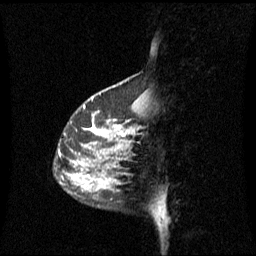
Breast MRI (dynamic contrast-enhanced), one sagittal slice; slice 19 of 60 in the series (ordered by position); dynamic contrast-enhanced series, image 2 of 3 at this slice position (ordered by acquisition); 1.5 T; TE 4.2 ms, TR 8.4 ms; 256 × 256 image matrix, field of view 240 × 240 mm. Patient: female, 42 years. From the clinical record (not read from this slice): setting: breast cancer imaged before/during neoadjuvant chemotherapy; receptor status: HR-positive, HER2-negative.
Annotated regions visible in this slice (semi-automatic segmentation, software-assisted and operator-edited):
- analysis volume of interest (the breast-tissue region the enhancement analysis was run in; not a lesion): bounding box [x1, y1, x2, y2] px = [68, 100, 137, 193]
- tumour enhancement mask (voxels above the 70 % enhancement threshold inside the analysis volume of interest): [92, 126, 129, 137]